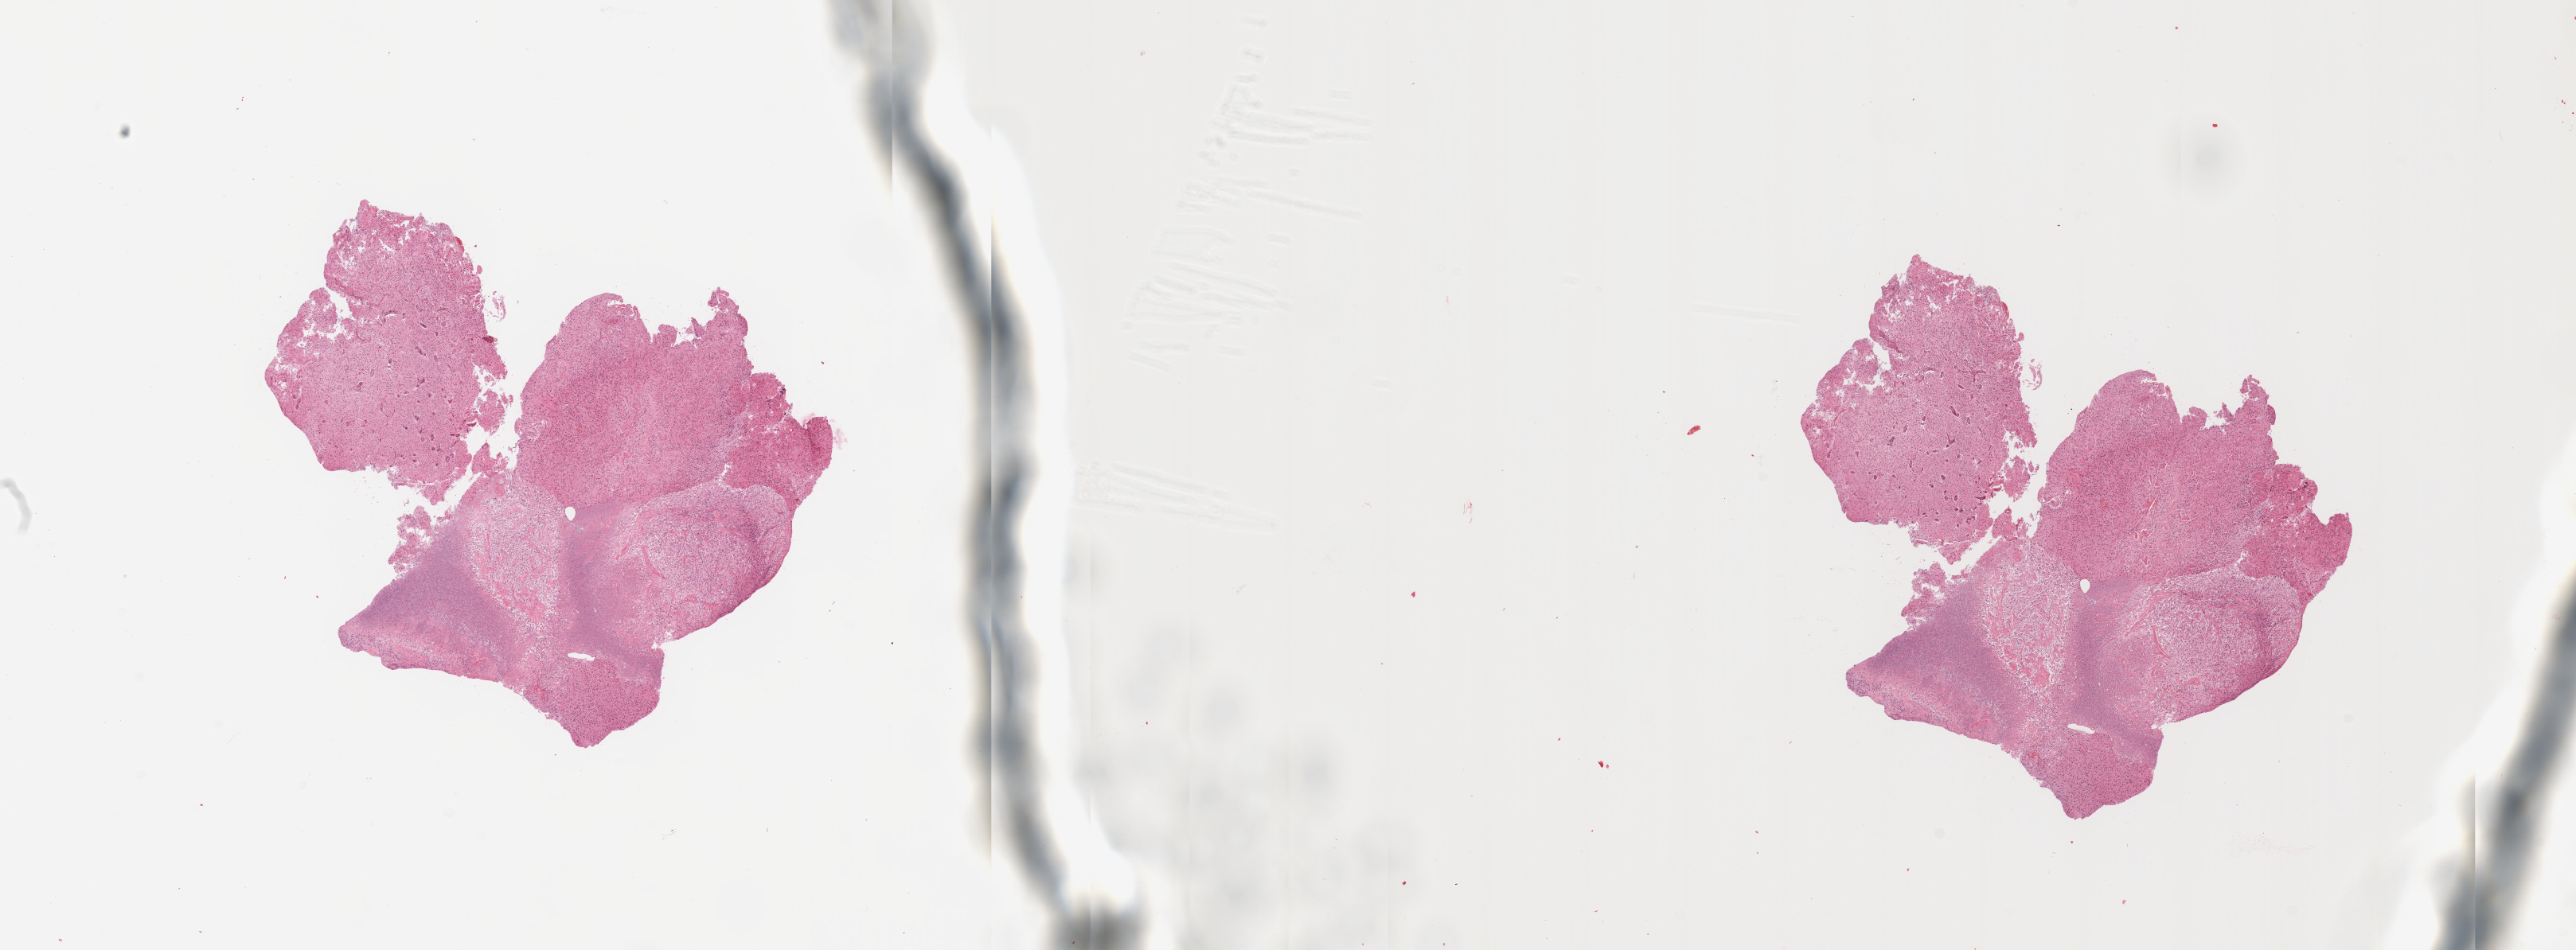
Whole-slide histology image, H&E, a low-resolution overview of the entire scanned area, about 25.6 x 9.4 mm (from a 20x scan), tumour tissue sample, sampled site: frontal lobe. 73-year-old female patient. Composition of this section per pathologist review: tumour nuclei 70%, necrosis 25%.
Diagnosis: Glioblastoma.